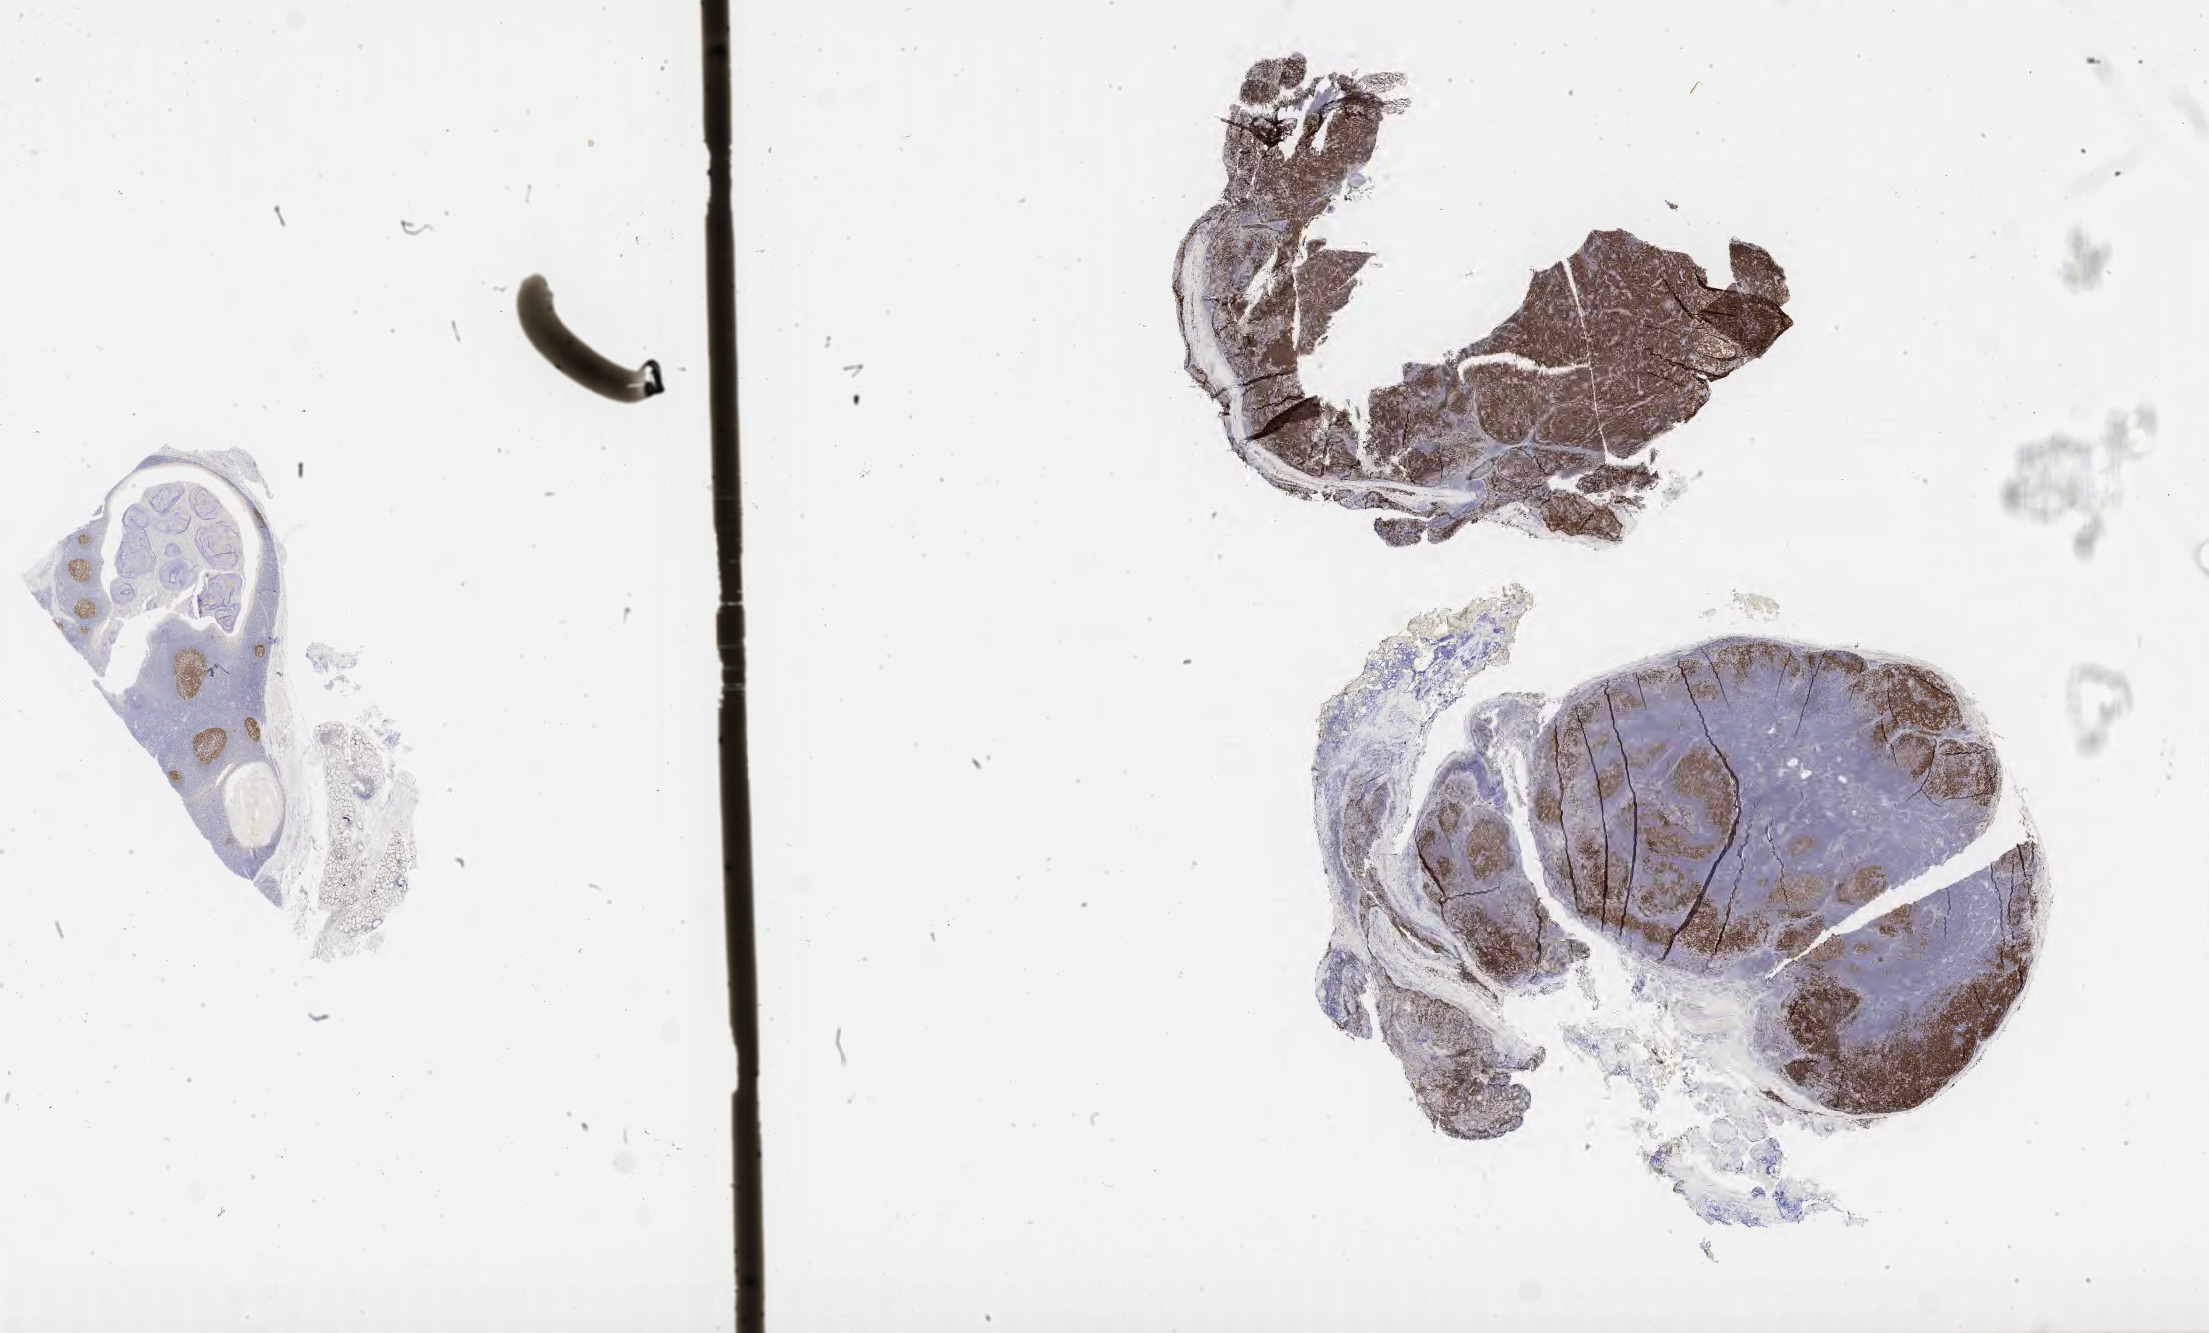
Immunohistochemistry (IHC) whole-slide image stained for BCL6 — a low-resolution overview of the entire scanned area, about 35.7 x 21.6 mm, tumor tissue. Patient male; 25 years old.
• diagnosis: Burkitt lymphoma, NOS